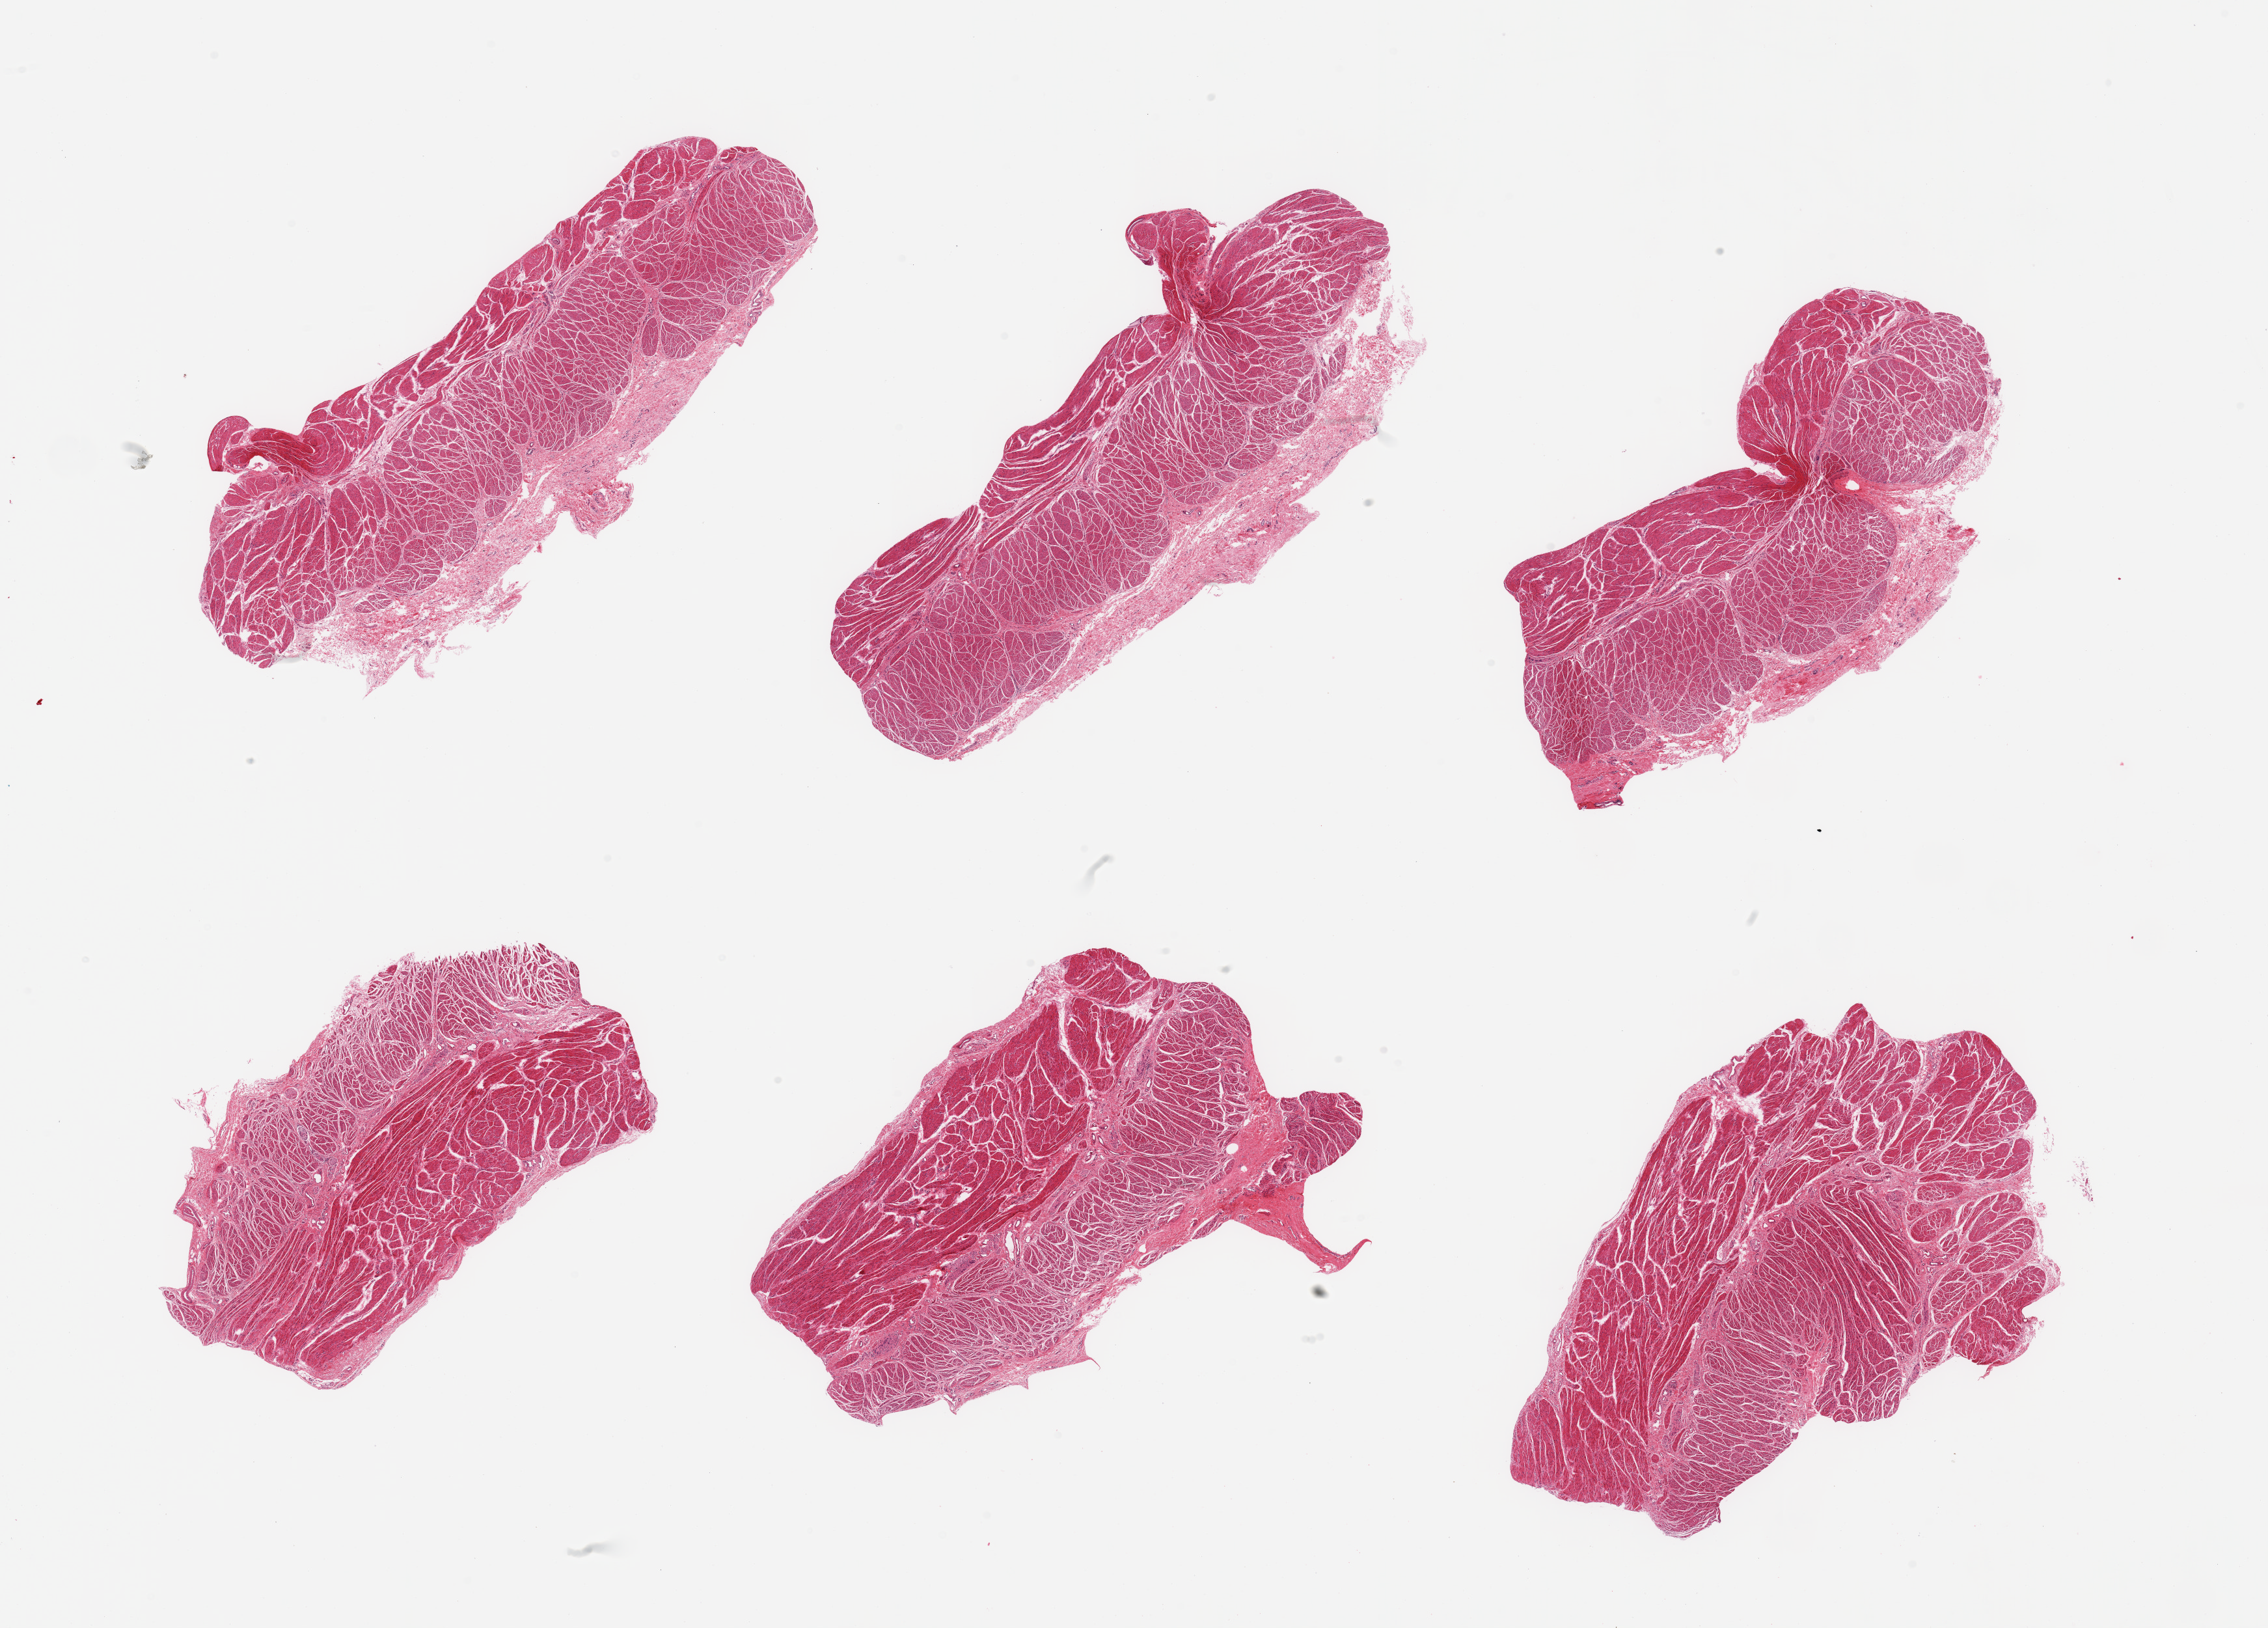
Digitized haematoxylin and eosin-stained section, brightfield — low-resolution overview of the scanned area, about 27.6 x 19.8 mm (slide scanned at 20x); PAXgene-fixed paraffin-embedded (PFPE) section; target tissue: esophageal muscle; tissue donor sample.
Reviewer comment on this tissue sample: 6 pieces; well dissected; no lesions.